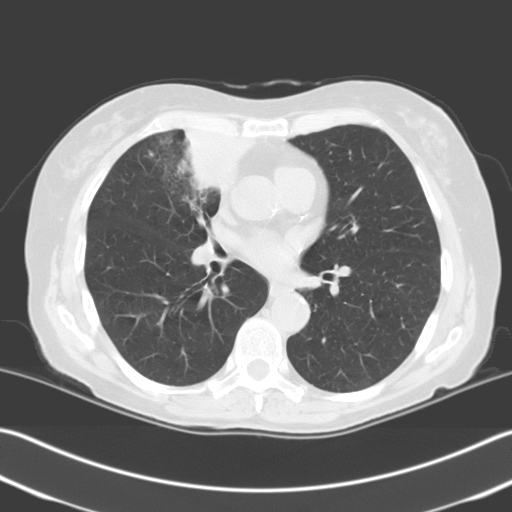
Low-dose screening chest CT, one axial slice; position 115 of 204 along the scan axis; lung window (W 1500 / L -600 HU); 3.2 mm slice thickness; 512 × 512 image matrix, field of view 348 × 348 mm.
Annotated regions visible in this slice (expert manual segmentation):
- lesion 1 (tumor, upper lobe of right lung): bounding box (x1, y1, x2, y2) in pixels: (179, 131, 251, 192)